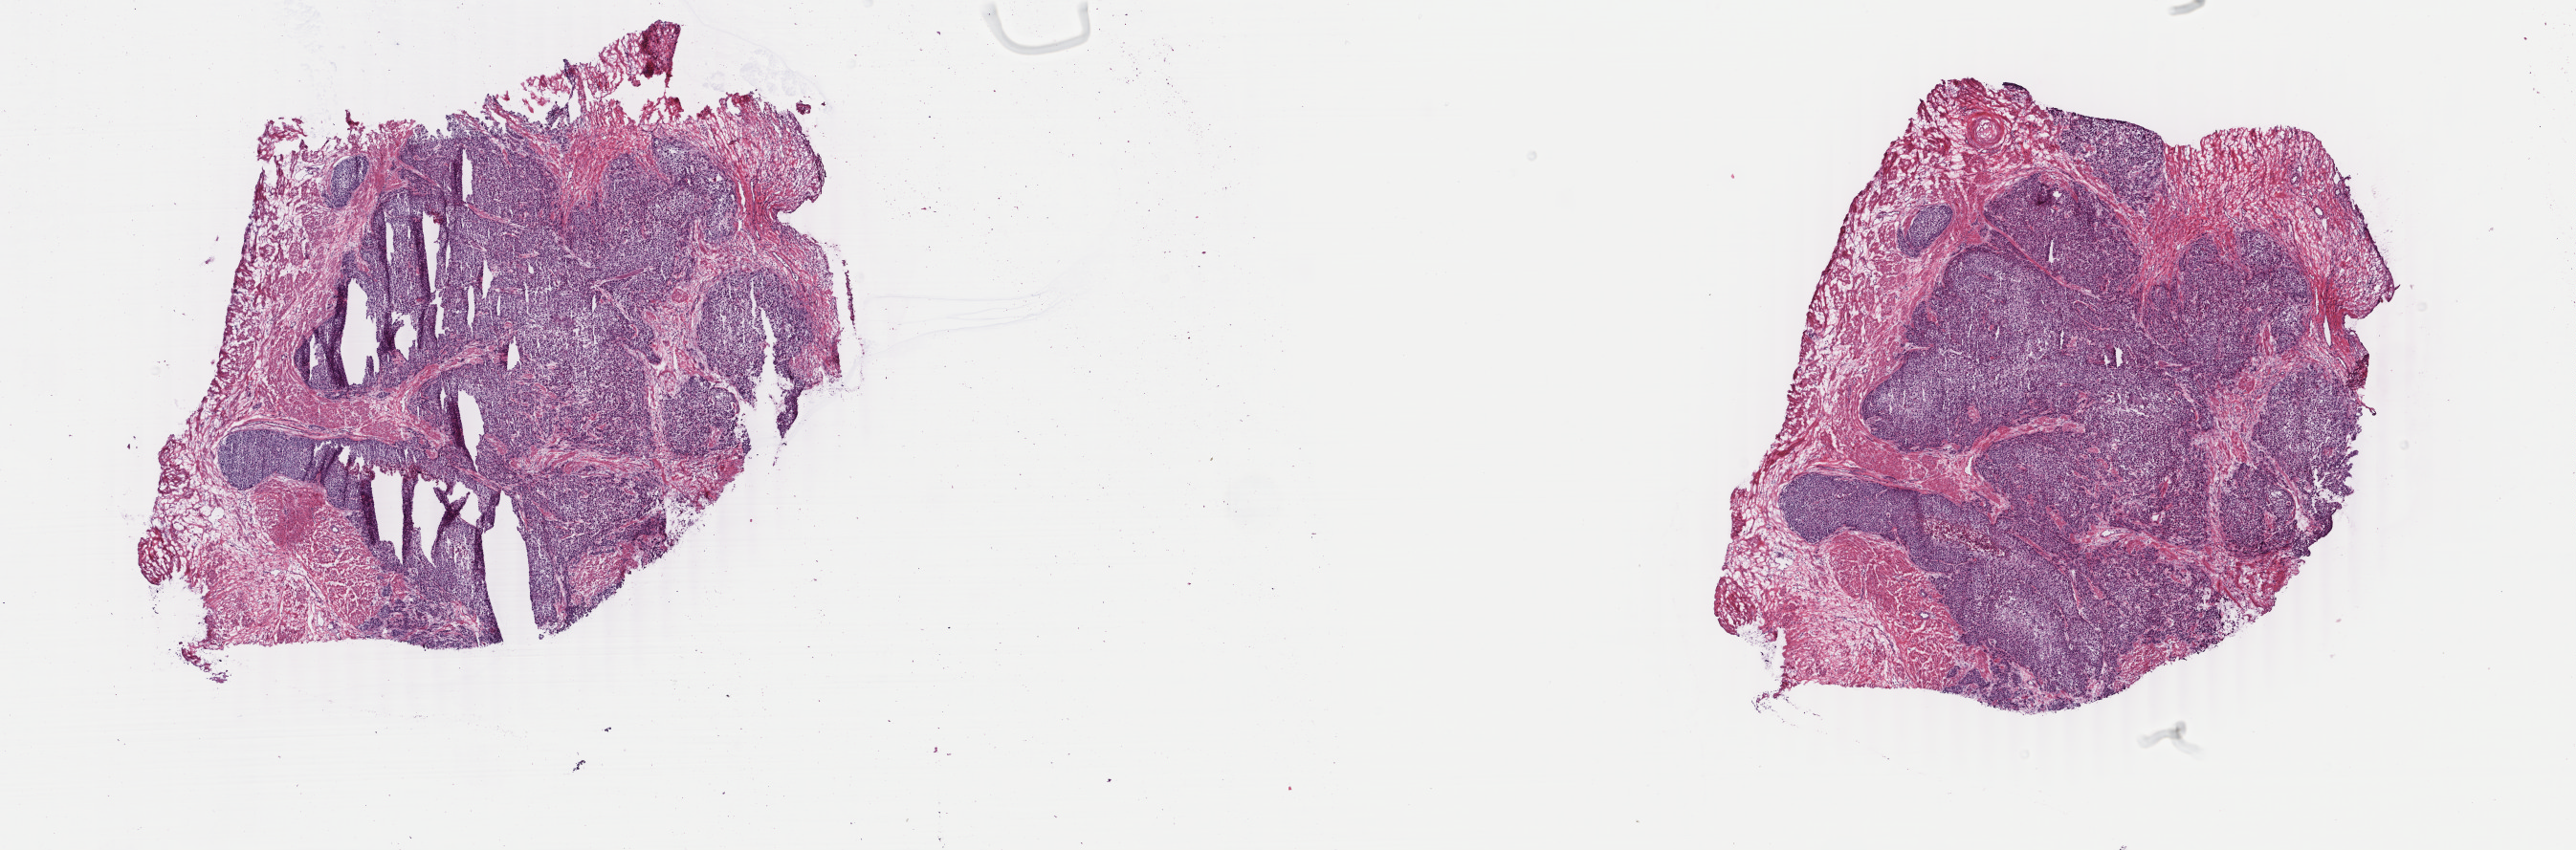
H&E-stained whole-slide image — a low-resolution overview of the entire scanned area, about 21.4 x 7.1 mm, frozen section, bladder, primary tumour sample. Male, age 77 years at initial diagnosis. Histologic grade: high grade. Composition of this section per pathologist review: tumour cells 60%, tumour nuclei 75%, normal cells 35%, stromal cells 2%, necrosis 3%. Infiltration values recorded for this section: lymphocyte infiltration 1%, monocyte infiltration 0%, neutrophil infiltration 2%.
* AJCC pathologic stage: IV (6th edition)
* diagnosis: Transitional cell carcinoma
* TNM: T4b N2 M0